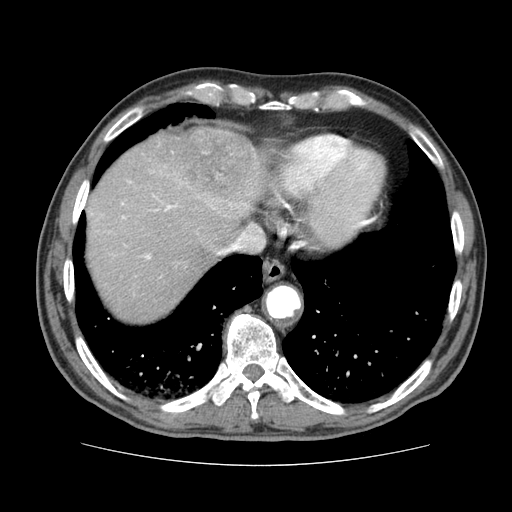
Contrast-enhanced abdominal CT (liver protocol), one axial slice; slice 67 of 79 in the series (ordered by position); reconstruction kernel STANDARD; 120 kVp; soft-tissue window (W 400 / L 40 HU); 2.5 mm slice thickness; 512 × 512 image matrix. From the clinical record (not read from this slice): diagnosis: hepatocellular carcinoma (patient treated with transarterial chemoembolisation; whether this scan precedes or follows treatment is not stated here); TNM stage (as recorded): Stage-I; Child-Pugh class: A; tumour nodularity: uninodular.
Annotated regions visible in this slice (semi-automatic segmentation, software-assisted and operator-edited):
- liver parenchyma outside the tumour (the mass and vessels are separate outlines, so this box may not span the whole liver): bounding box [x1, y1, x2, y2] px = [86, 128, 274, 322]
- mass: [149, 126, 265, 220]
- liver vessels: [122, 203, 177, 259]